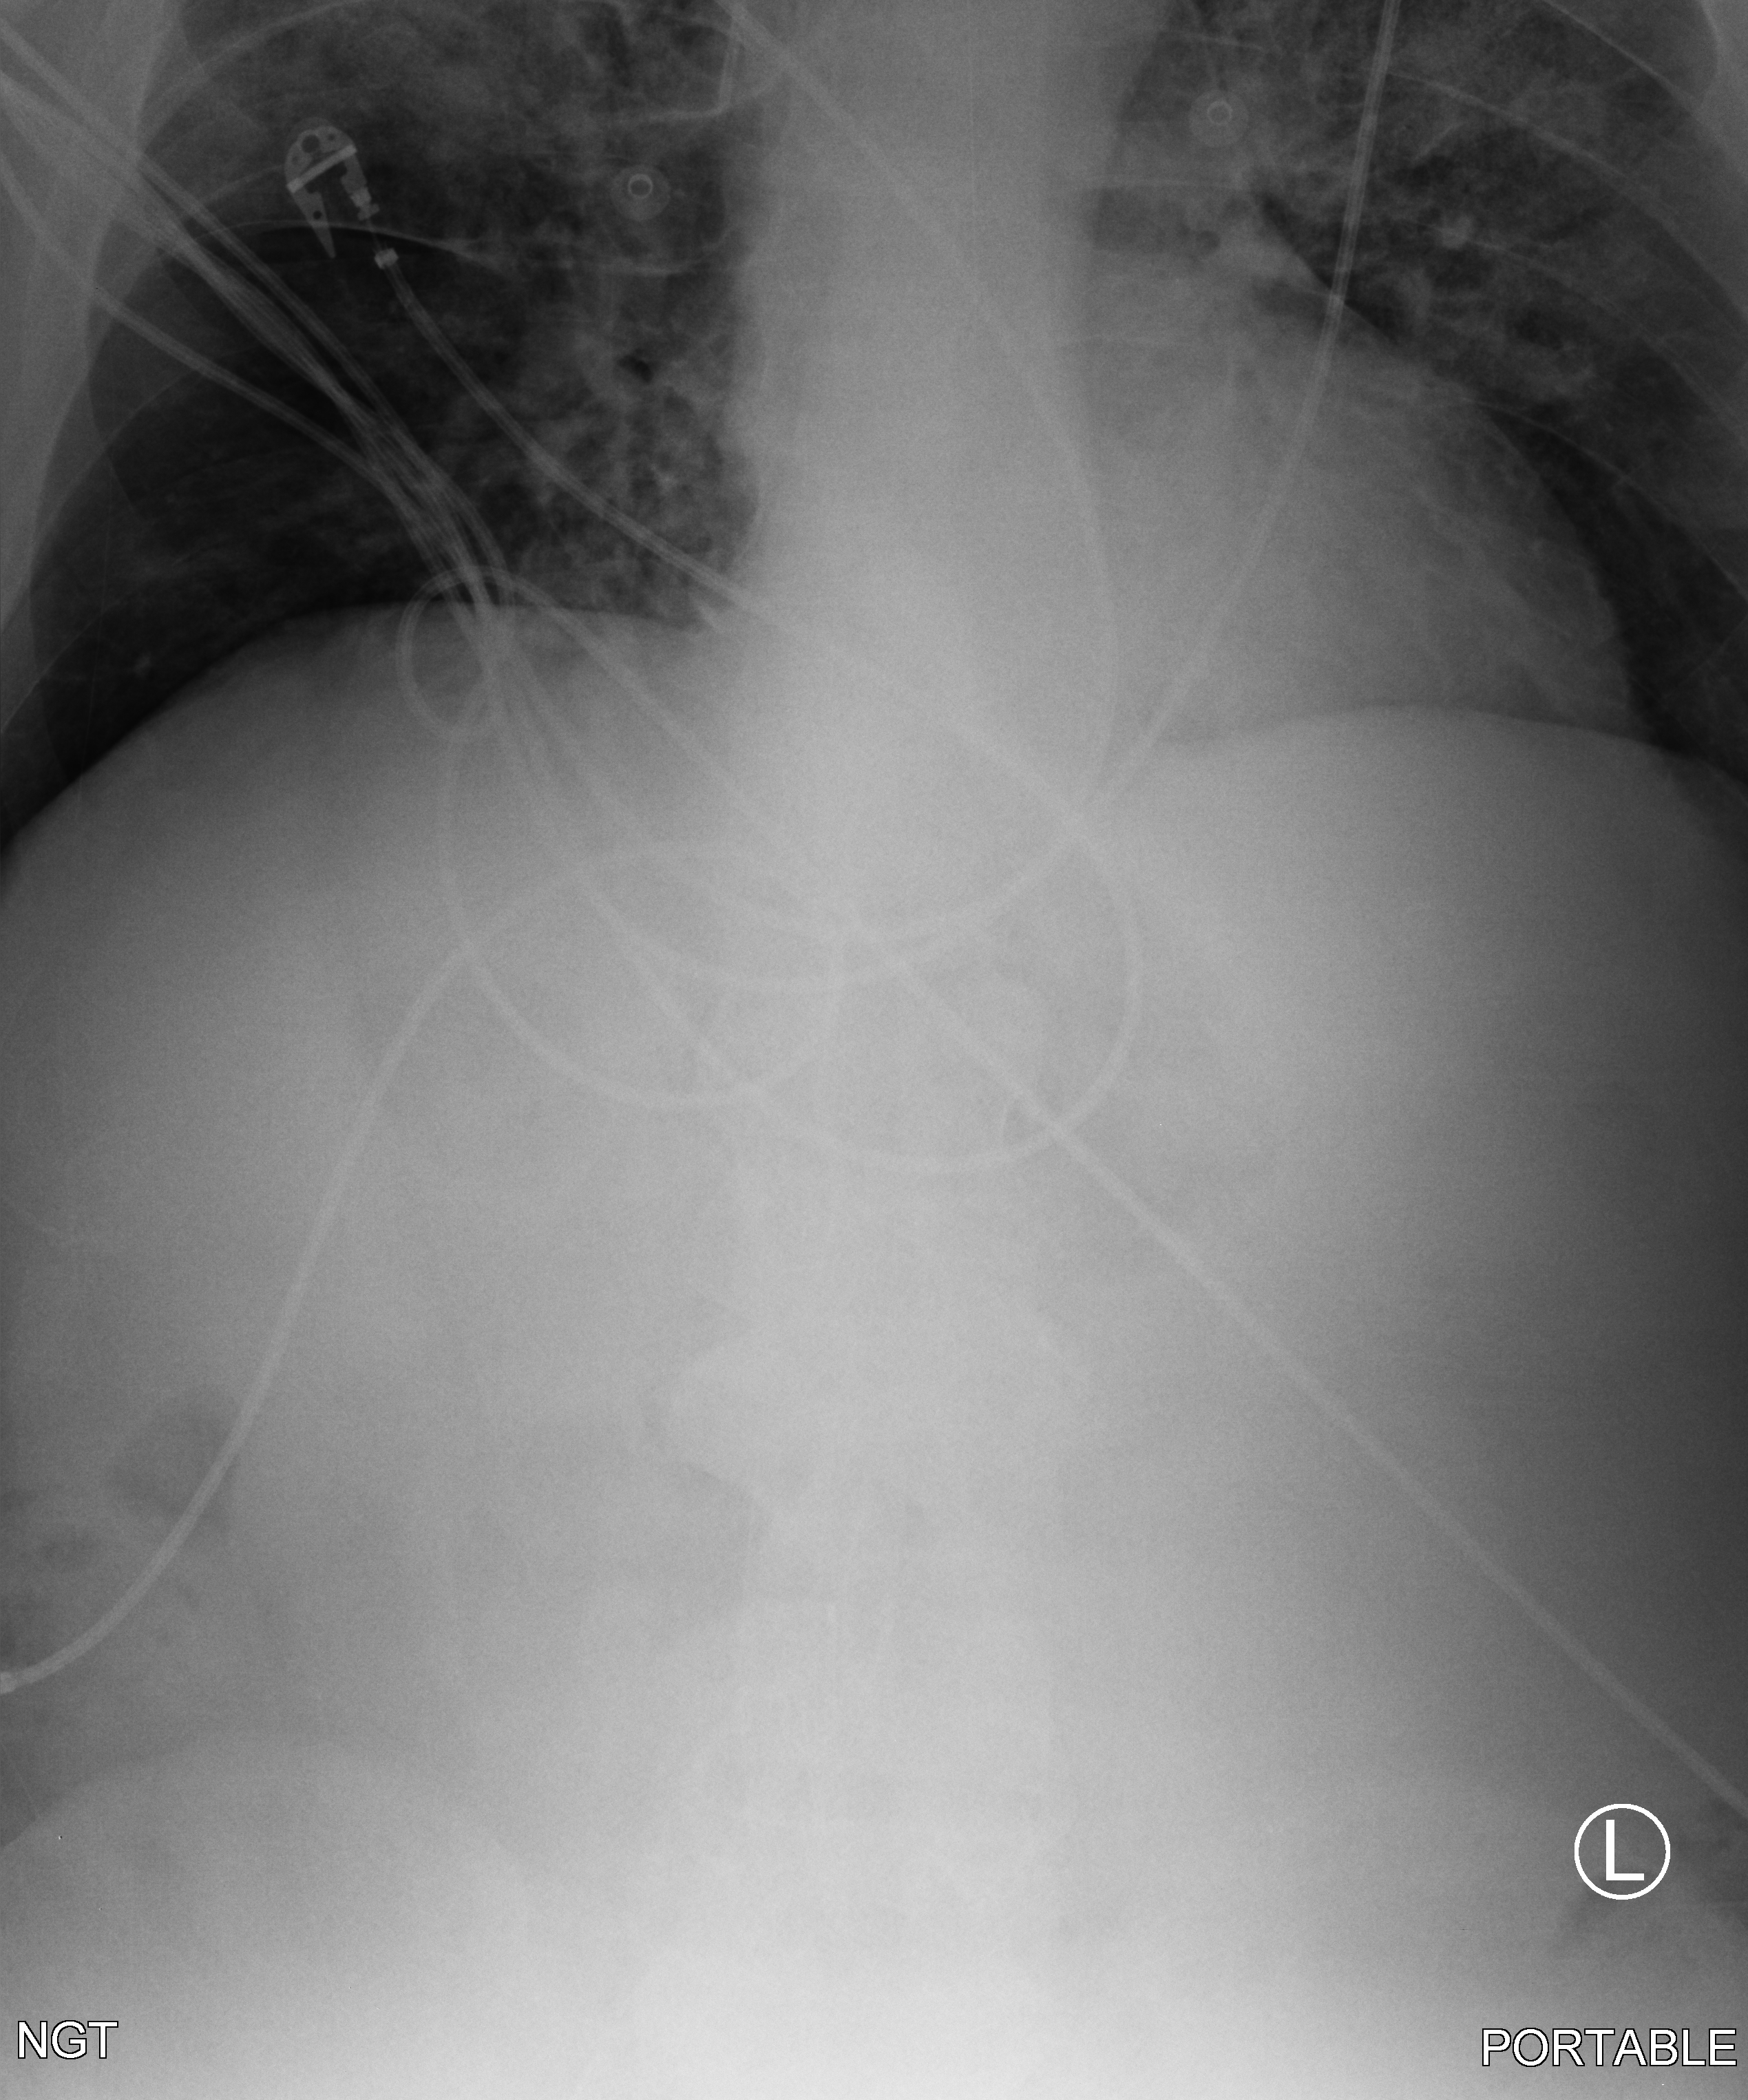
Bedside chest radiograph (computed radiography); anteroposterior (AP) projection. Male patient hospitalised with COVID-19, age 75–90 years.
From the hospital-stay record, not from the radiograph (when in the stay this image was taken is not recorded): mechanically ventilated during this hospital stay: yes; chronic kidney disease (admission record): no.